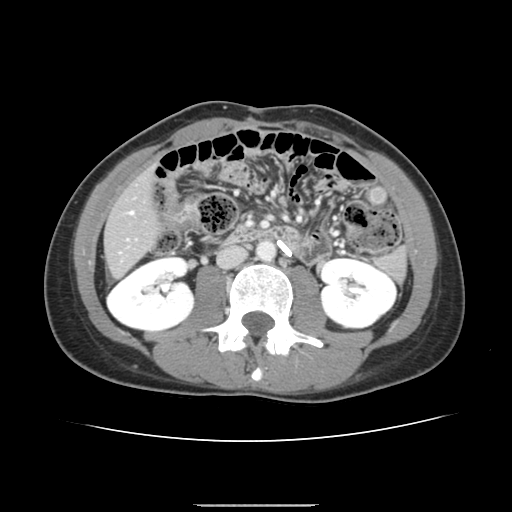
Contrast-enhanced abdominal CT, one axial slice; position 48 of 150 along the scan axis; 120 kVp; intravenous contrast given; soft-tissue window (W 400 / L 40 HU); 2.5 mm slice thickness; 512 × 512 image matrix, field of view 324 × 324 mm. Female patient, age 32 years. Case-level facts recorded for this patient, not image findings: diagnosis: colorectal cancer liver metastases, imaged before liver resection; multiple liver metastases: yes; largest metastasis: 0.7 cm; disease in both lobes: no.
Outlined on this slice (outlined manually by an expert reader):
- hepatic veins: bounding box <130,211,133,214> (left, top, right, bottom; pixels)
- liver: <106,173,157,276>
- planned liver remnant (the part of the liver to remain after resection): <106,174,157,275>